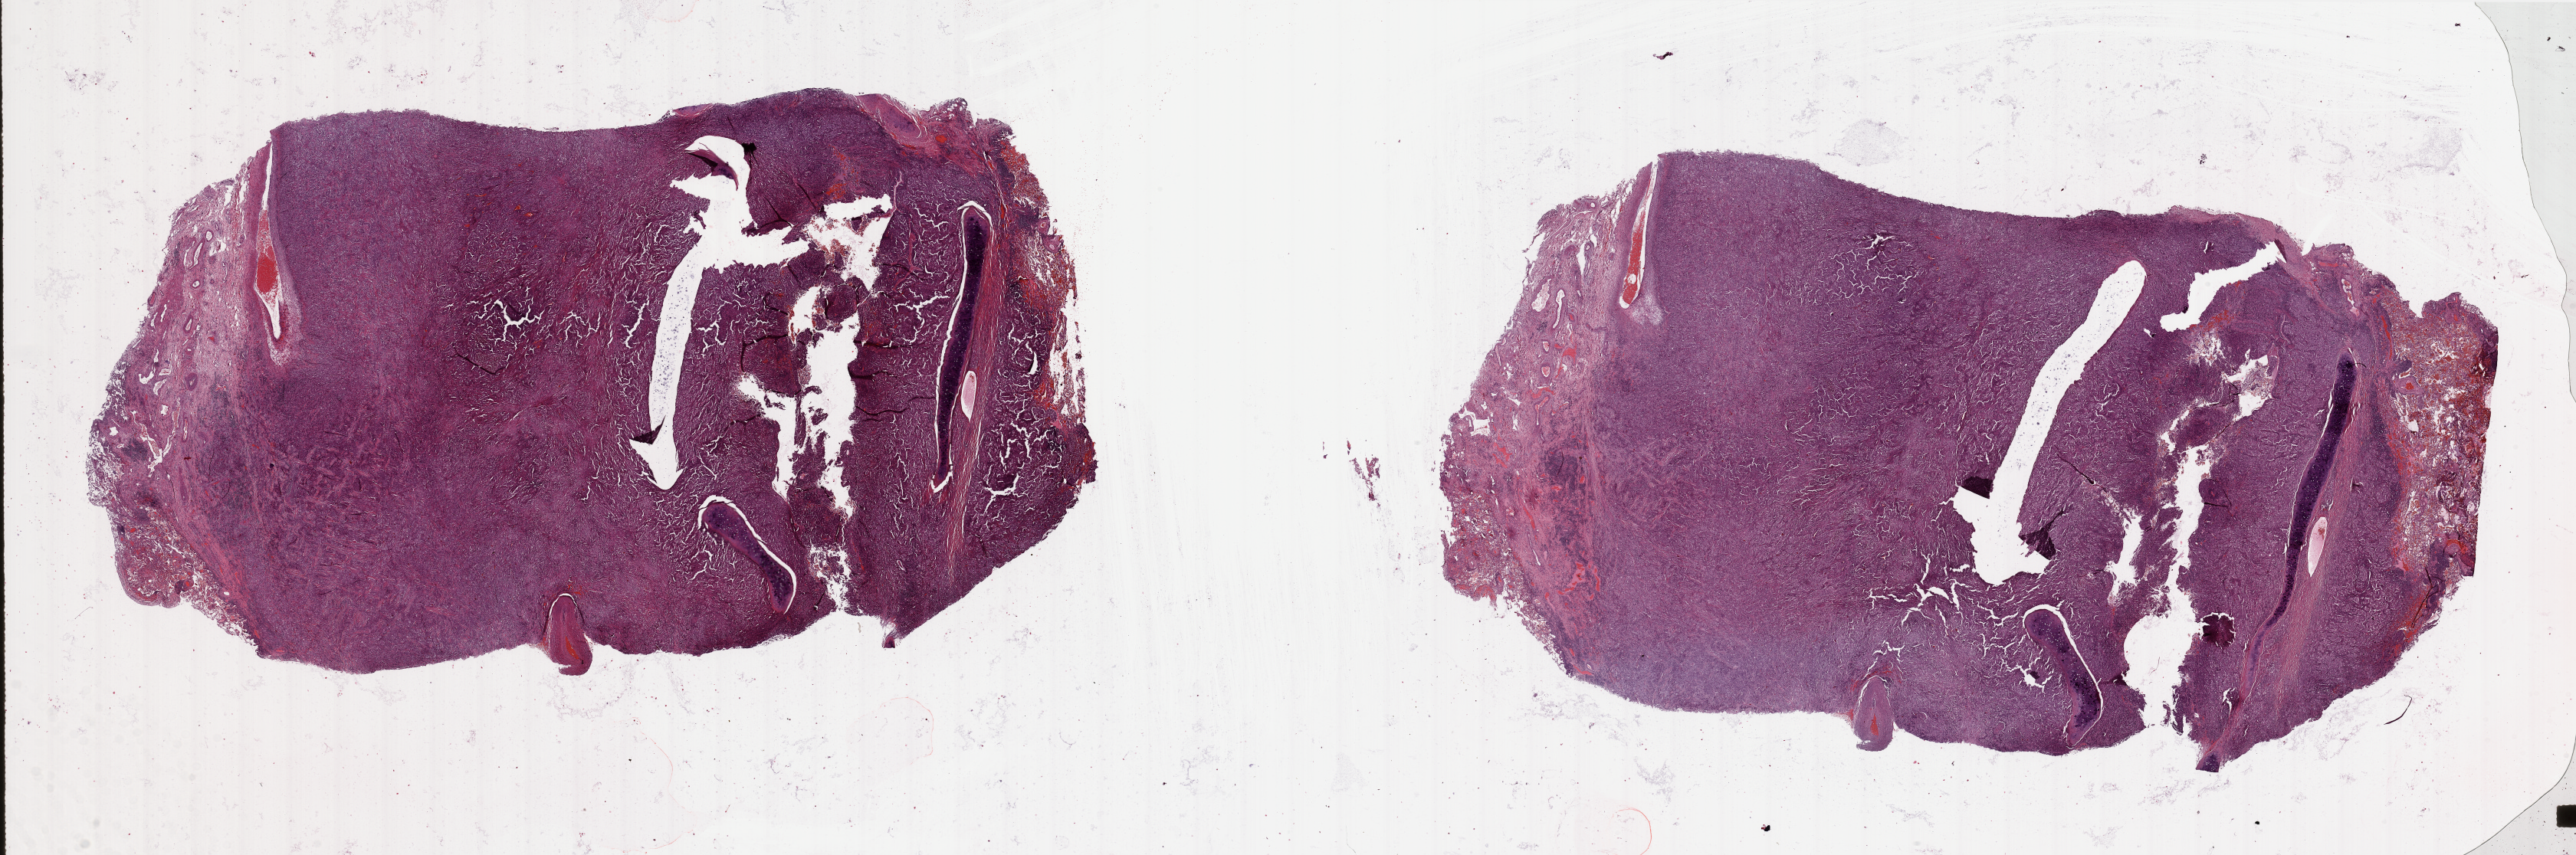
Hematoxylin and eosin (H&E) stained whole-slide image, low-resolution overview of the scanned area, about 53.2 x 17.7 mm, tumour tissue sample, sampled site: lung. 72-year-old male patient. Histologic grade: G3 (poorly differentiated). Composition of this section per pathologist review: tumour nuclei 80%, necrosis 3%.
AJCC pathologic stage: IB. Histologic diagnosis: Adenocarcinoma, NOS. Primary tumour site (as recorded): left upper lobe.